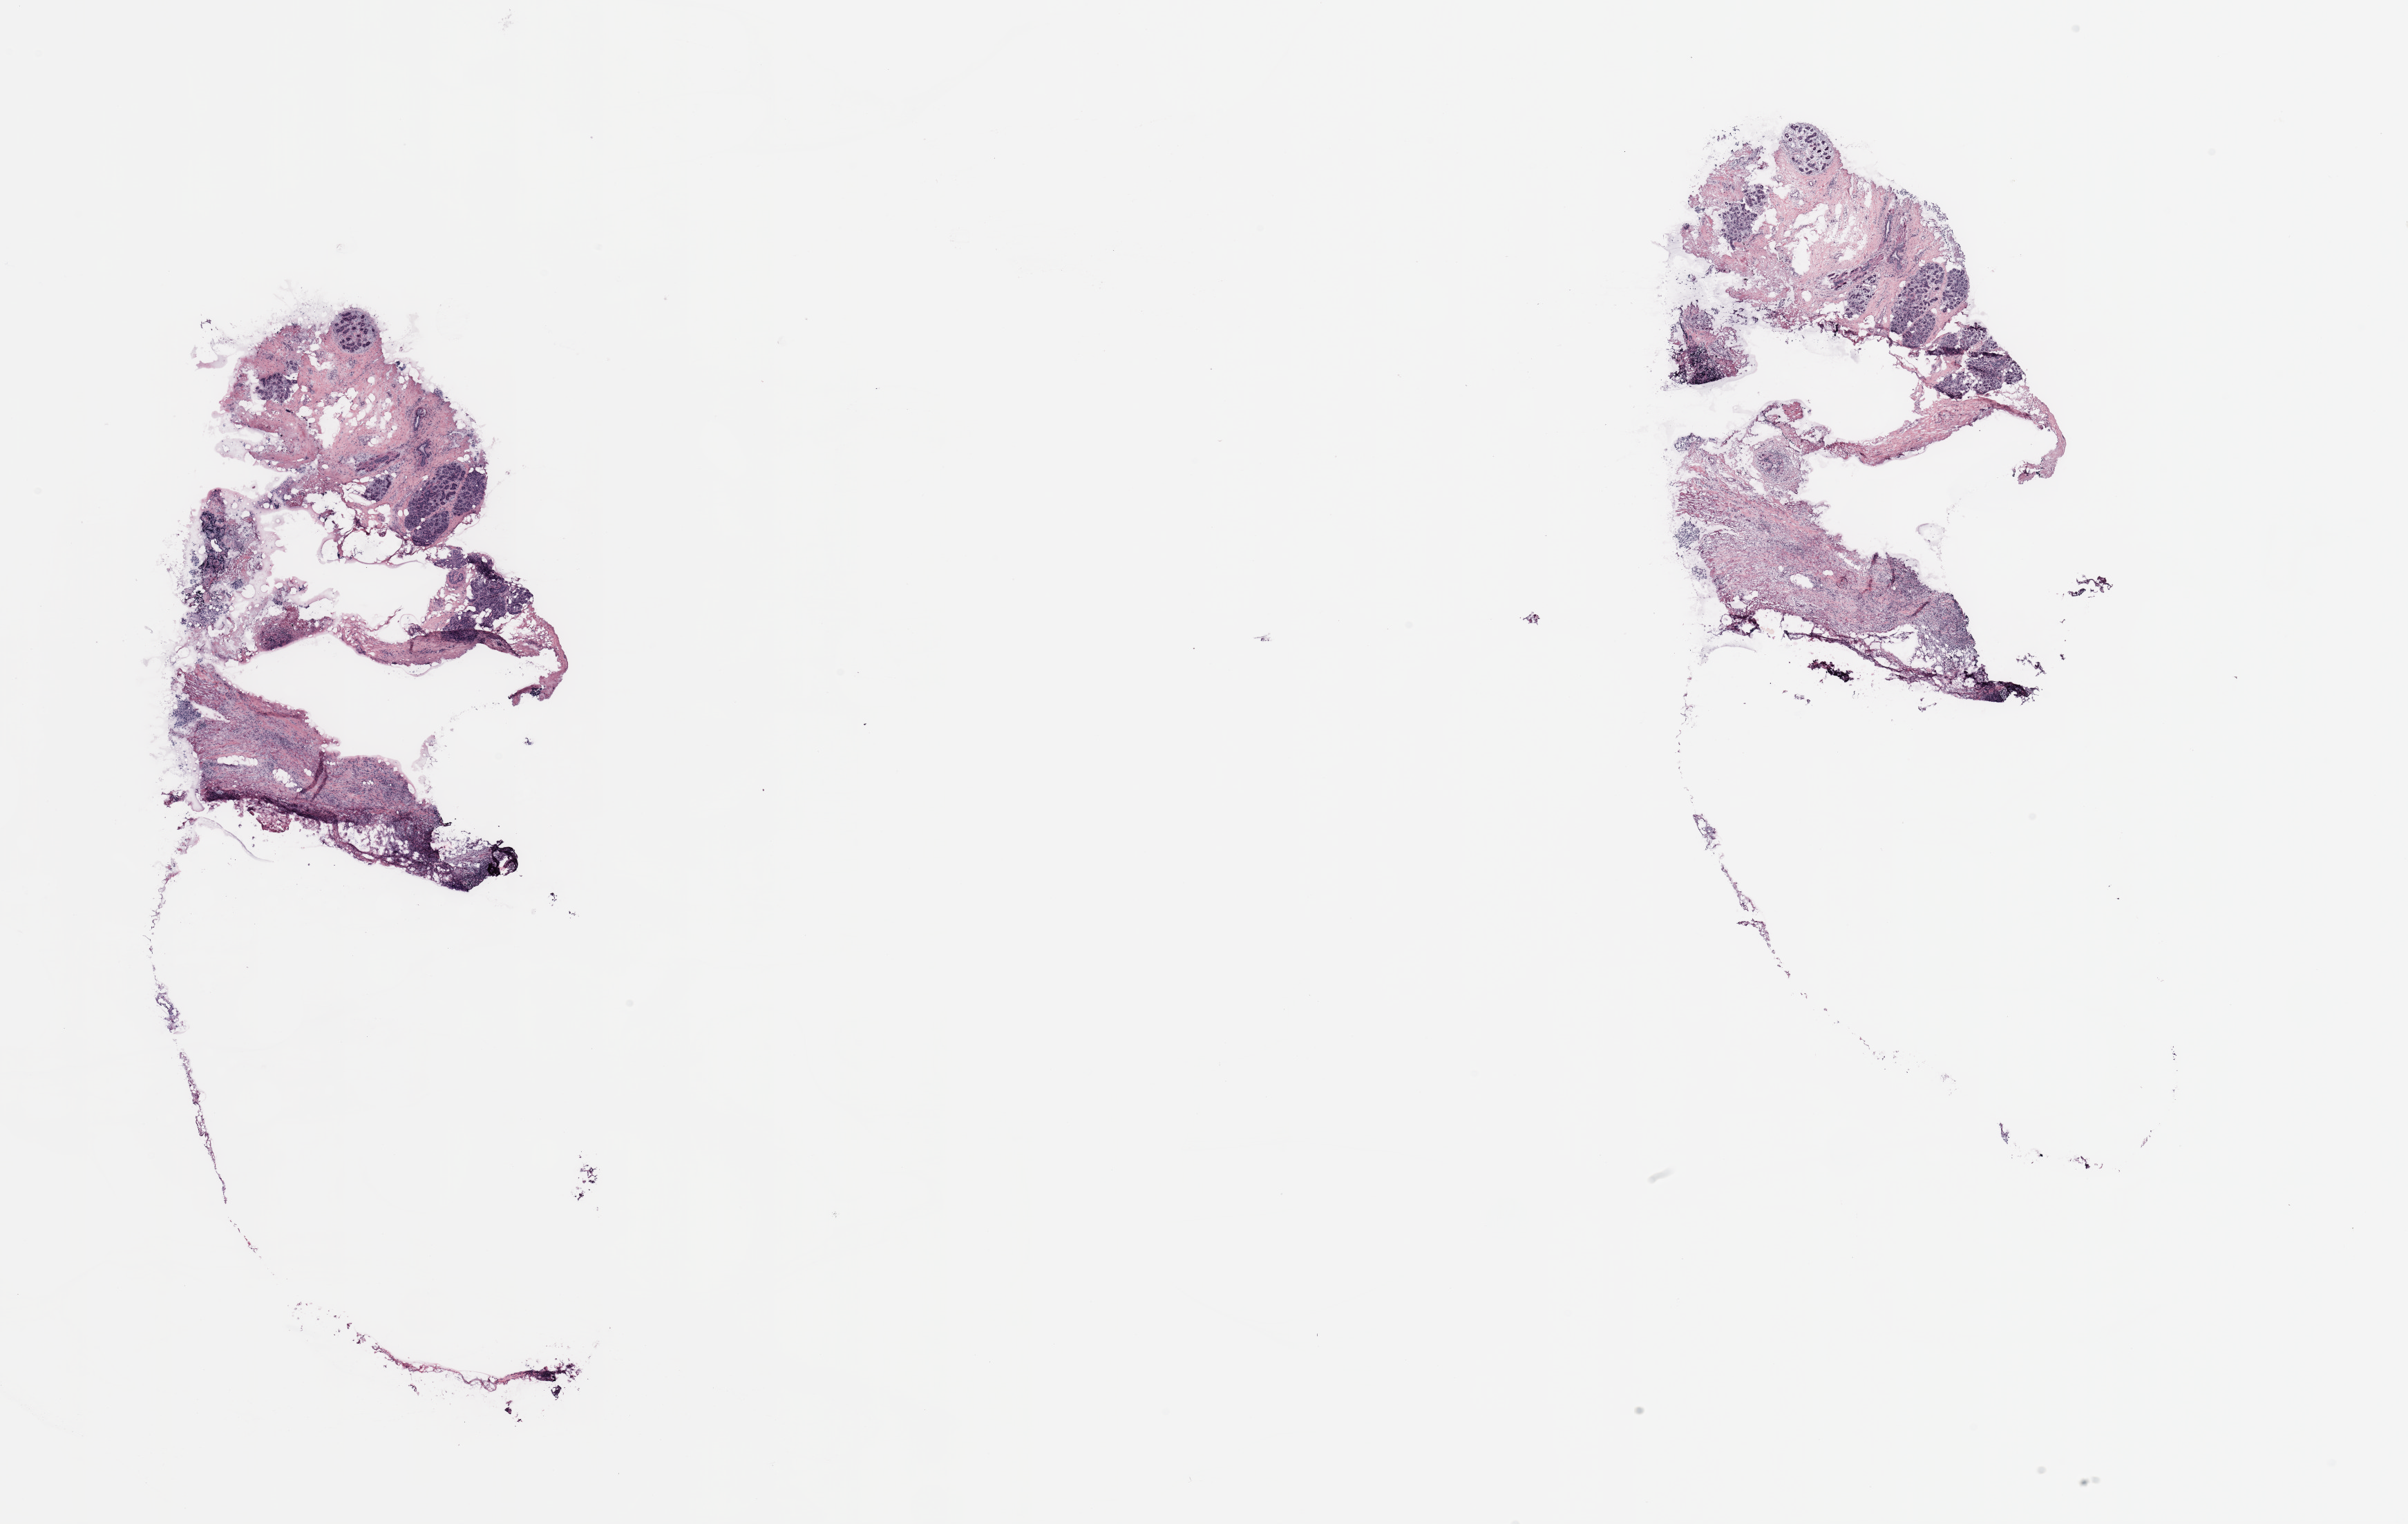
H&E whole-slide image — whole scanned area (about 27.6 x 17.4 mm, from a 20x scan) shown as a low-resolution overview.
Specimen: breast, tissue type not recorded.